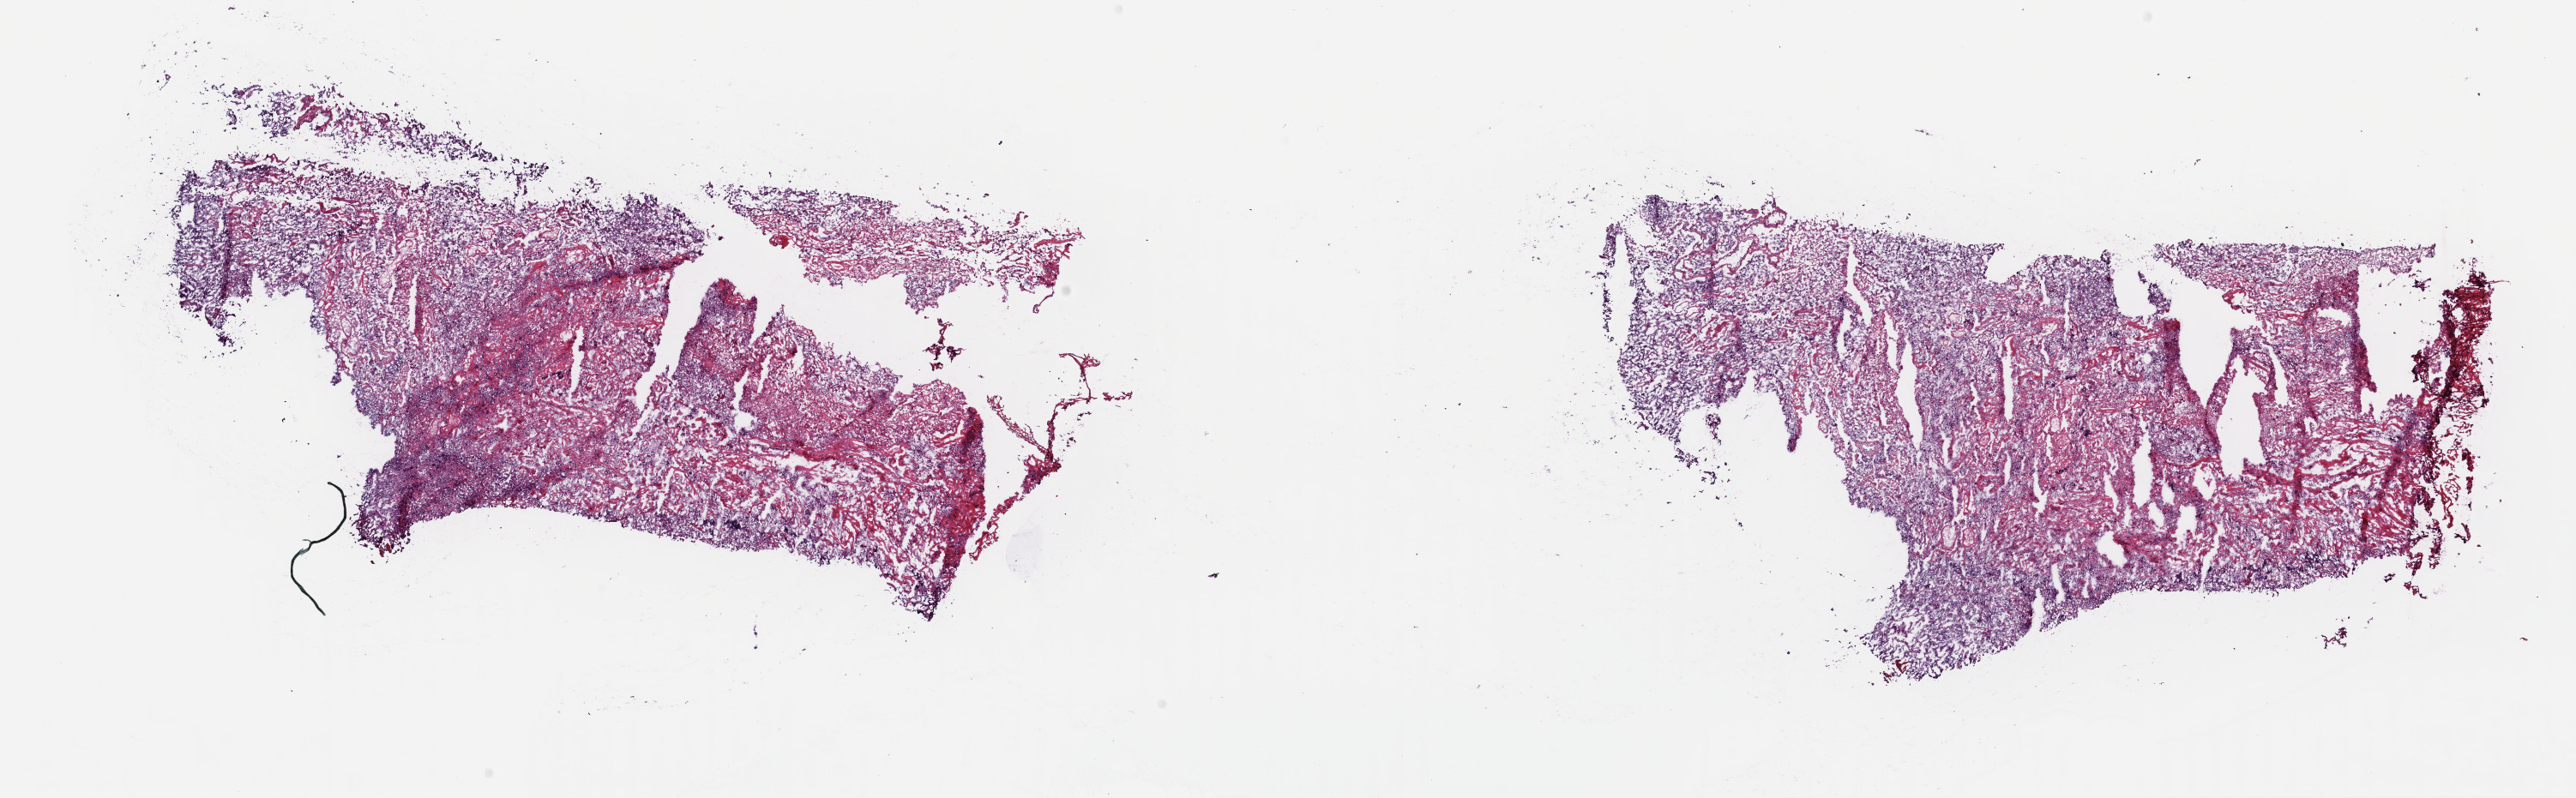
Whole-slide histology image, H&E, shown as a low-resolution overview of the whole scanned area (about 23.7 x 7.4 mm, slide scanned at 40x), frozen section, sample: primary tumour, uterus. Female, age 74 years at initial diagnosis. Histologic grade: G3 (poorly differentiated). Composition of this section per pathologist review: tumour cells 100%, tumour nuclei 75%, normal cells 0%, stromal cells 0%, necrosis 0%. Inflammatory infiltration, as recorded: lymphocyte infiltration 0%, monocyte infiltration 0%, neutrophil infiltration 0%.
FIGO stage: IB. Diagnosis: Serous cystadenocarcinoma, NOS.